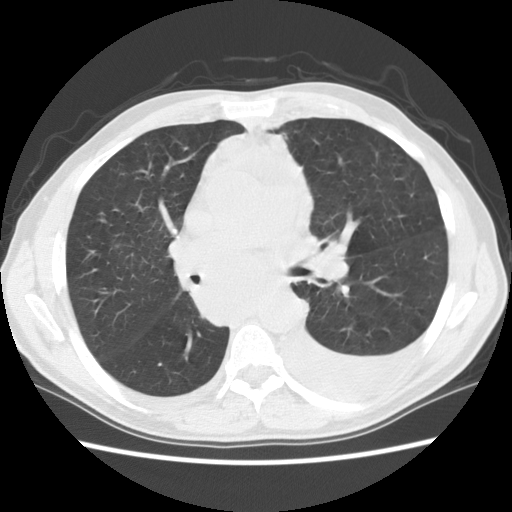
Axial slice from a low-dose chest CT screening exam. First (baseline) screen. Lung window (W 1500 / L -600 HU). 2.5 mm slice thickness. 140 kVp. Slice 52 of 135 in the series. Male participant, aged 60 years at enrolment. Current smoker at enrolment.
• Expert-annotated lung lesion, bounding box <176,238,299,329> (left, top, right, bottom; pixels).
• No non-calcified nodule or mass ≥4 mm was recorded by the screening reader at this exam.
• Official screen result: negative screen, significant abnormalities not suspicious for lung cancer.
• Participant outcome: lung cancer diagnosed 12 days after this screen — squamous cell carcinoma, NOS, carina, poorly differentiated (G3), stage IV (AJCC 6th edition).